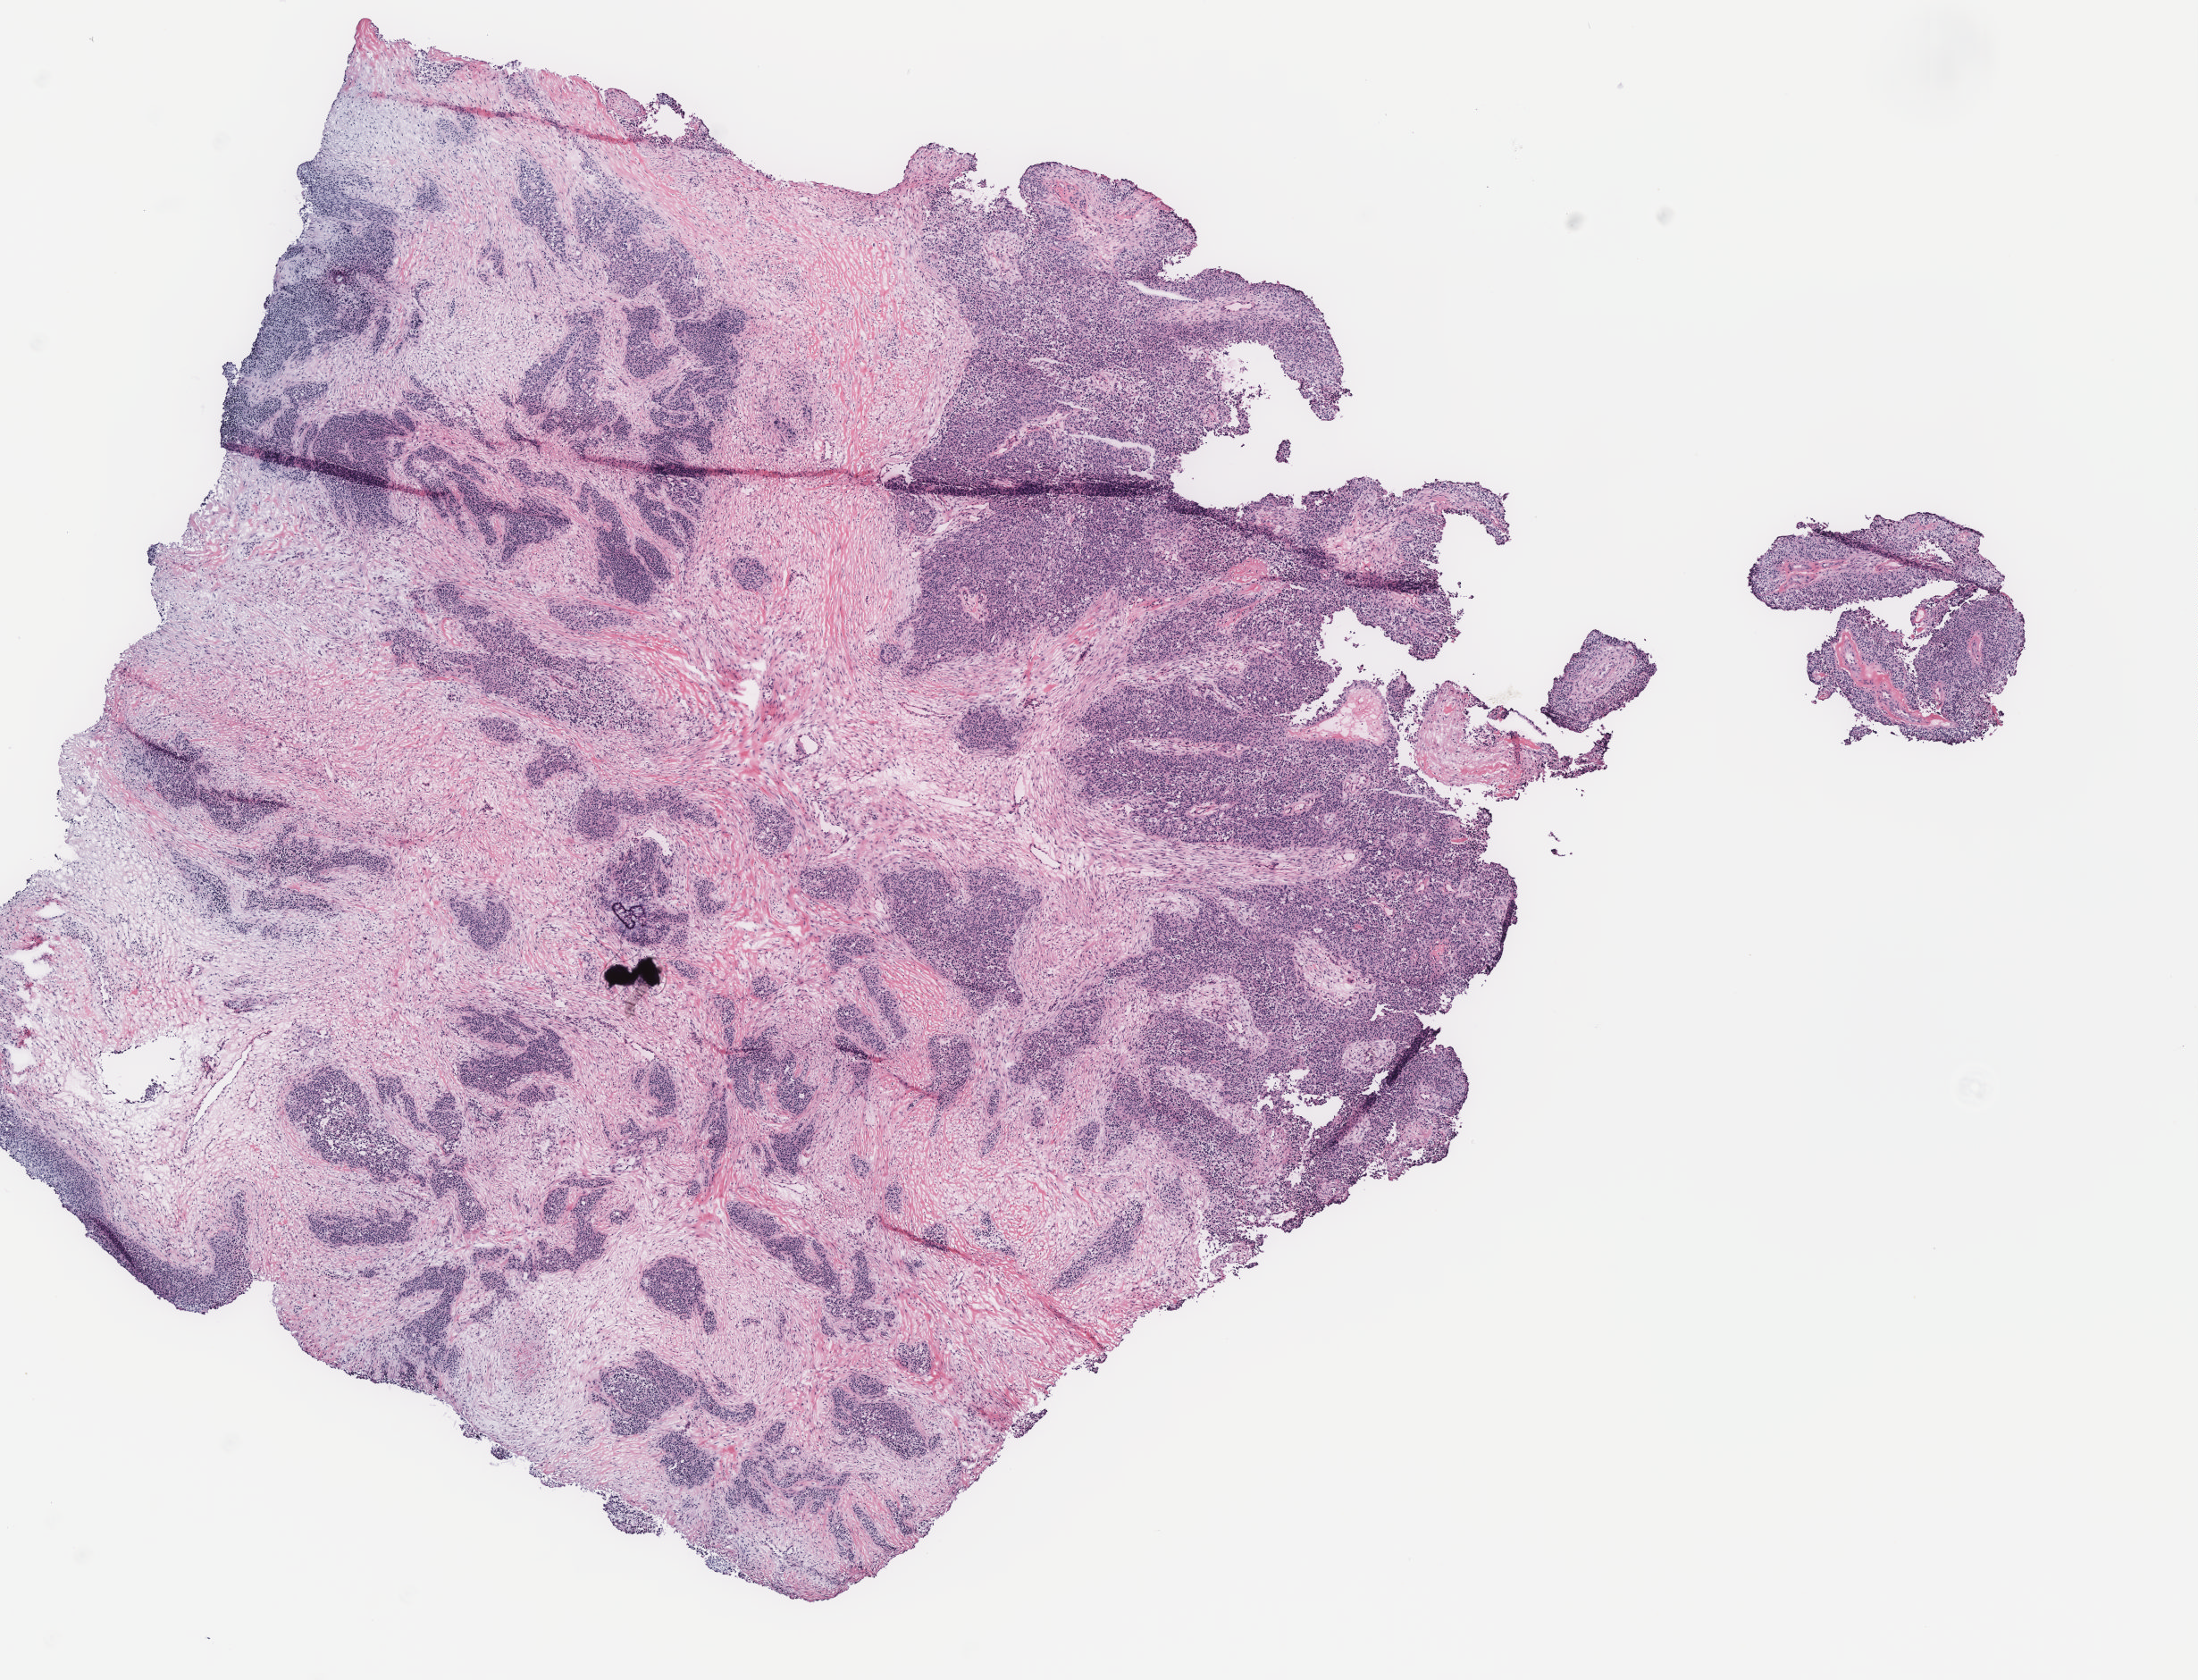
Digitized Hematoxylin and eosin (H&E) stained tissue section (whole slide) — shown as a low-resolution overview of the whole scanned area (about 9.8 x 7.5 mm); ovary, tissue type not recorded. Patient sex: female.
Patient diagnosis: Serous adenocarcinoma, NOS.